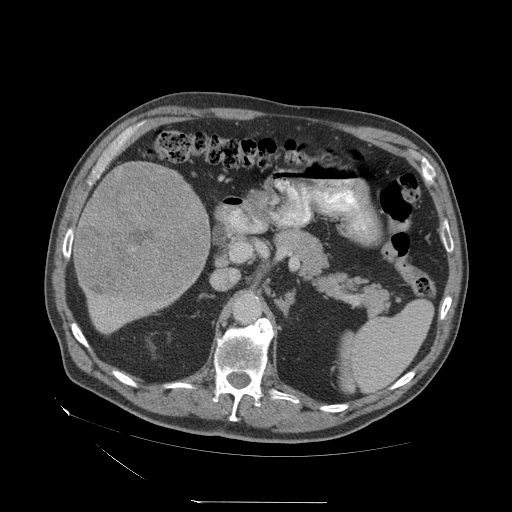
Contrast-enhanced abdominal CT (liver protocol), one axial slice; position 23 of 83 along the scan axis; reconstruction kernel STANDARD; soft-tissue window (W 400 / L 40 HU); 512 × 512 image matrix, field of view 460 × 460 mm. Case-level facts recorded for this patient, not image findings: diagnosis: hepatocellular carcinoma (patient treated with transarterial chemoembolisation; whether this scan precedes or follows treatment is not stated here); TNM stage (as recorded): Stage-I; Child-Pugh class: A; tumour differentiation: well differentiated; tumour nodularity: uninodular.
Outlined on this slice (semi-automatic segmentation, software-assisted and operator-edited):
- liver parenchyma outside the tumour (the mass and vessels are separate outlines, so this box may not span the whole liver): bounding box (x1, y1, x2, y2) in pixels: (72, 162, 210, 332)
- mass: (75, 161, 208, 301)